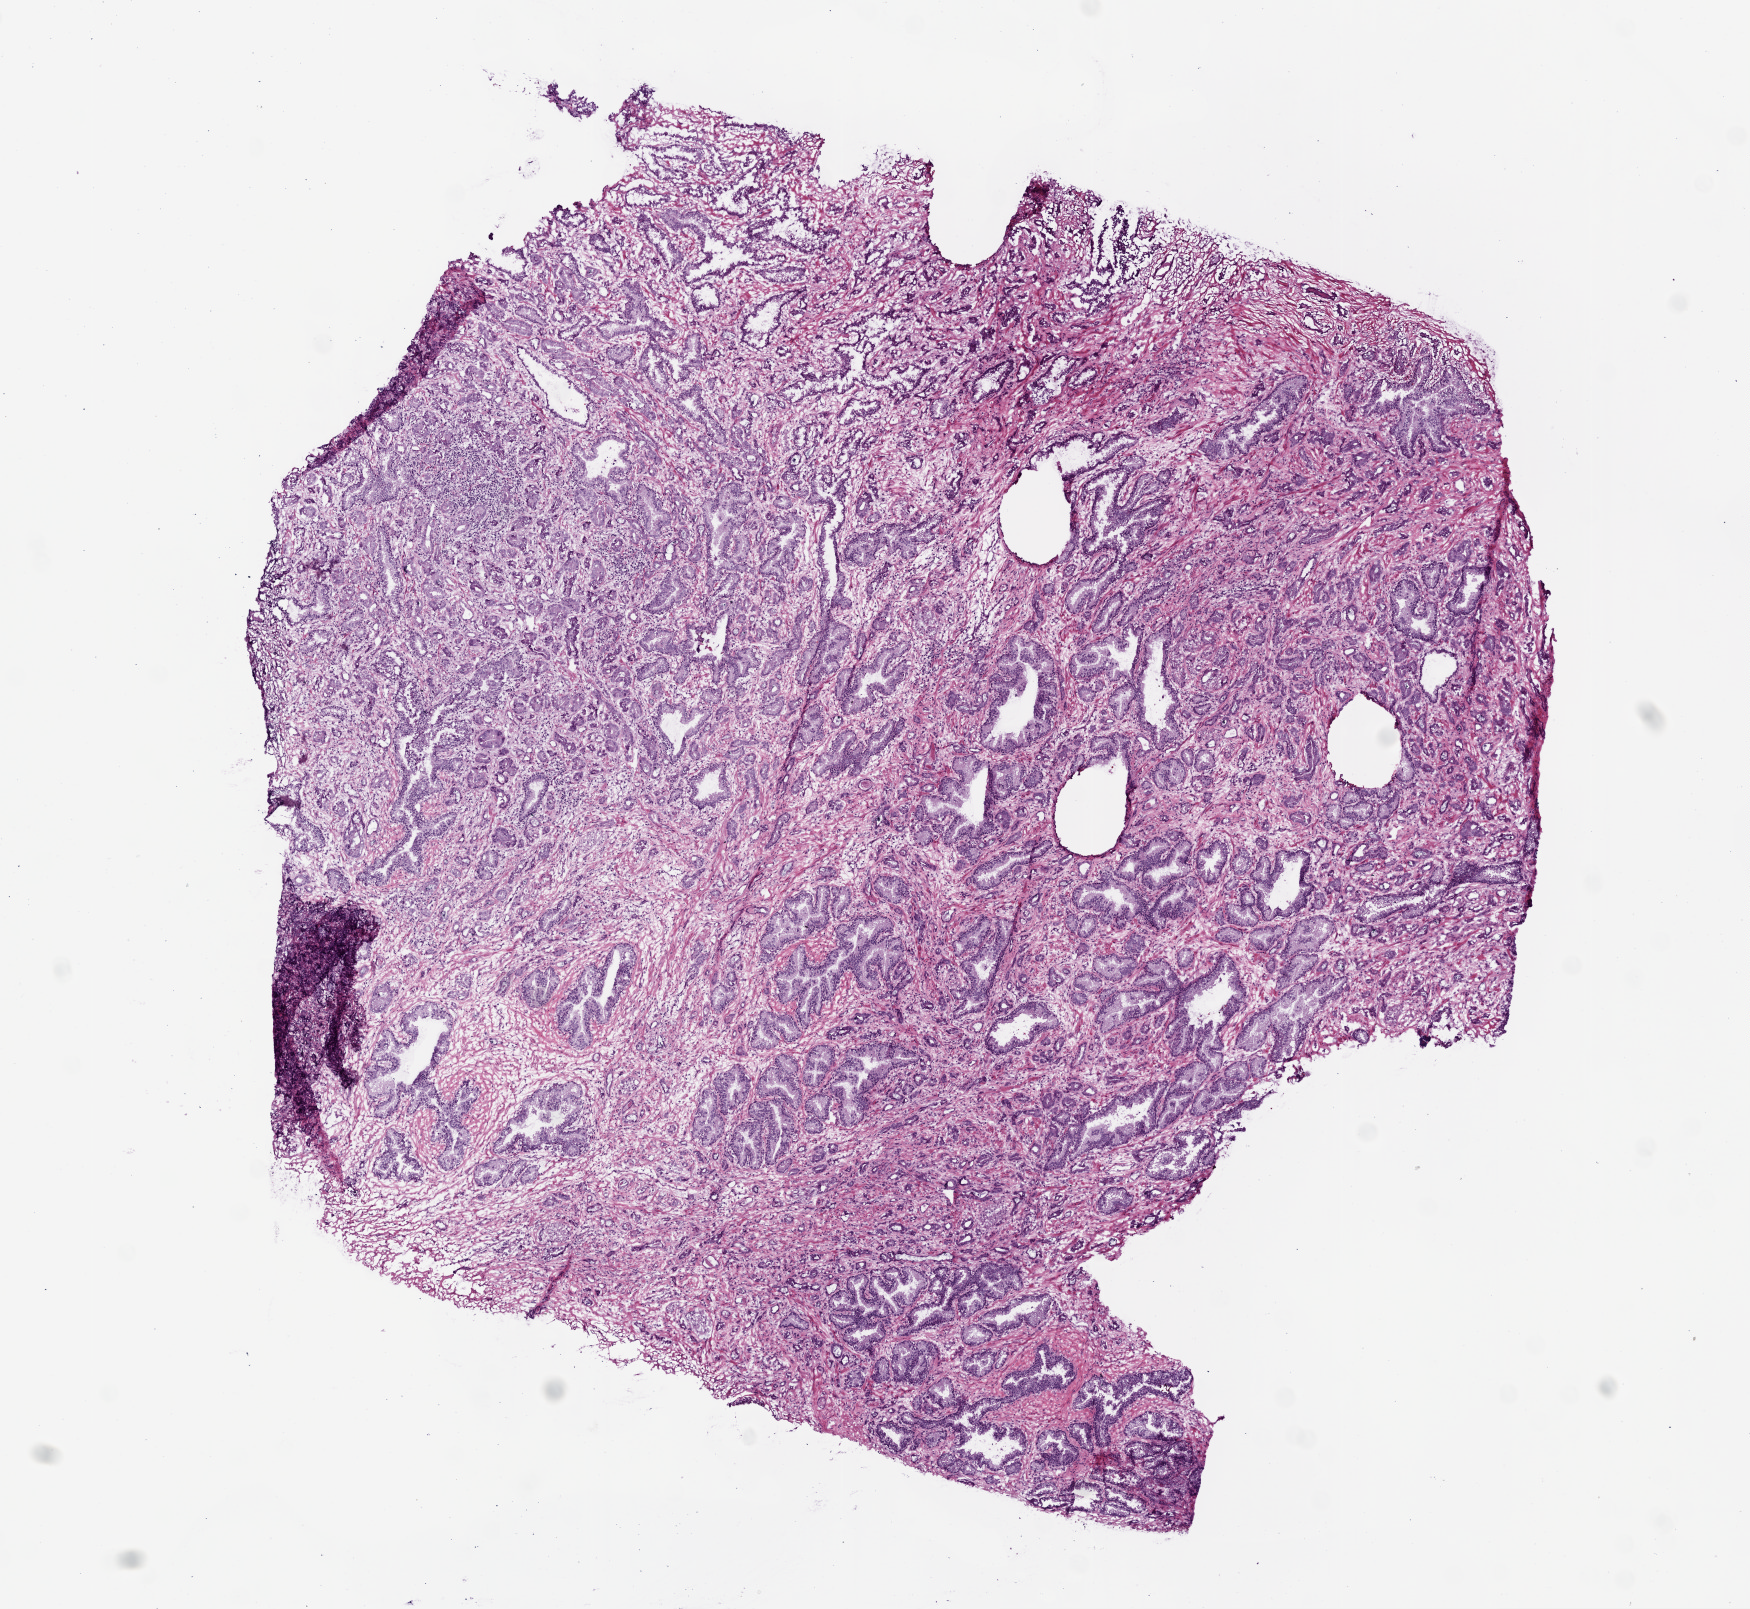
Hematoxylin and eosin (H&E) stained whole-slide image — shown as a low-resolution overview of the whole scanned area (about 7.0 x 6.5 mm, acquisition: 20x scan); frozen section; primary tumour sample from the prostate. Male patient; age at initial diagnosis 43 years.
Pathologic diagnosis: Acinar cell carcinoma (prostate gland).